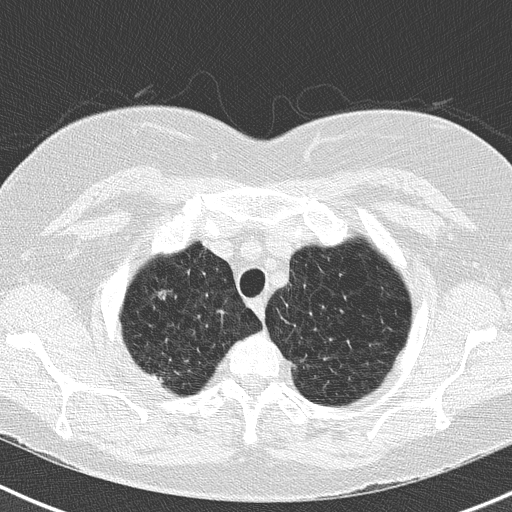
Low-dose screening chest CT, axial slice. Second annual screen. Lung window (W 1500 / L -600 HU). Lung (sharp) reconstruction kernel (B50f). Slice 31 of 183 in the series. Female, age 73 years at enrolment. Former smoker at enrolment.
• Lesion marked by an expert reader, bounding box <139,274,188,316> (left, top, right, bottom; pixels).
• The screening reader recorded 2 non-calcified nodules or masses ≥4 mm on this exam (right upper lobe, right upper lobe); which of them this box marks is not recorded.
• Official screen result: positive, no significant change: stable abnormalities potentially related to lung cancer, unchanged since the prior screening exam.
• Participant outcome: lung cancer diagnosed 250 days after this screen — adenocarcinoma, NOS, right upper lobe, moderately differentiated (G2), stage IB (AJCC 6th edition), 15 mm at pathology.